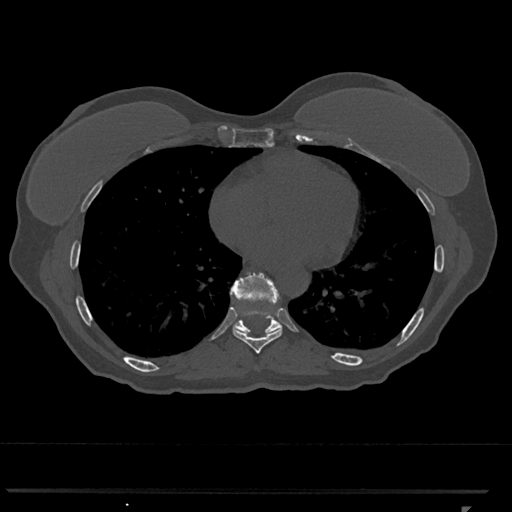
CT including the spine, one axial slice; slice 649 of 793 in the series (ordered by position); reconstruction kernel Br40s/3; 120 kVp; bone window (W 1800 / L 400 HU); 512 × 512 image matrix, field of view 380 × 380 mm. Patient: female, 62 years. Case-level facts recorded for this patient, not image findings: primary cancer: renal.
Outlined on this slice (semi-automatic segmentation, software-assisted and operator-edited):
- T8 vertebra: box from (x=233, y=309) to (x=282, y=354) px
- T9 vertebra: (x=230, y=273)–(x=282, y=335)